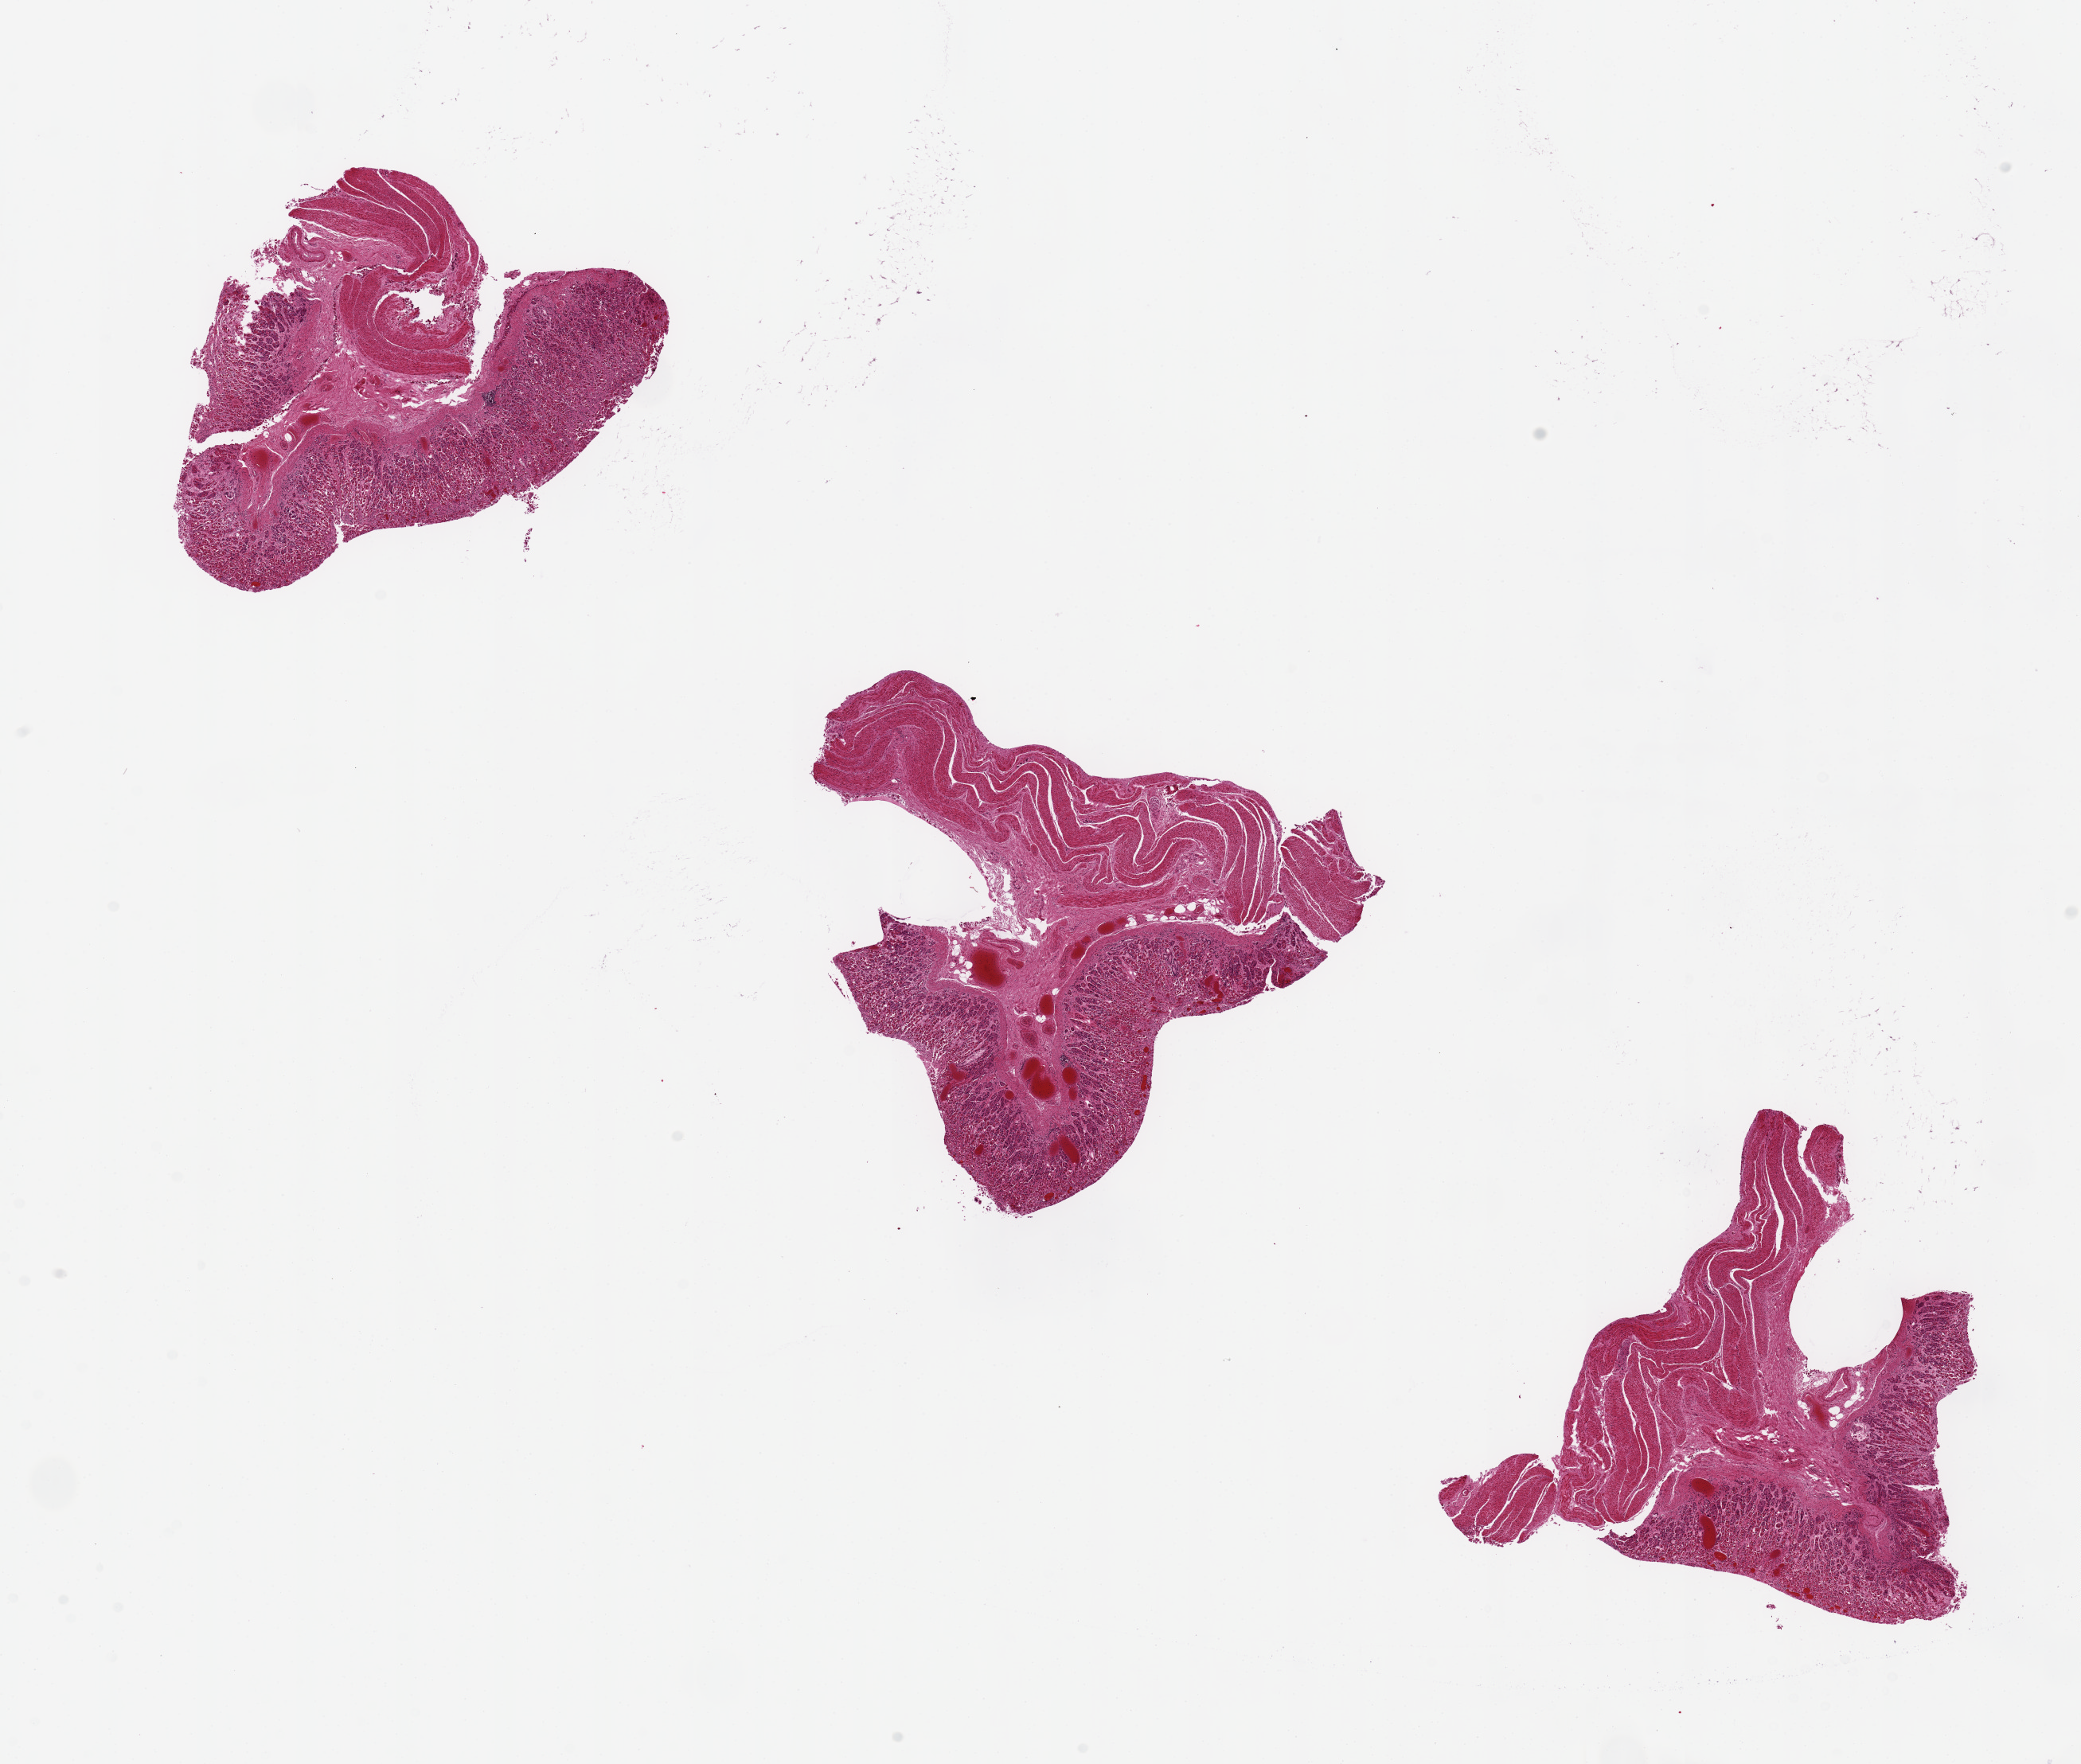
Whole-slide image, H&E stain, shown as a low-resolution overview of the whole scanned area (about 20.7 x 17.5 mm), PAXgene-fixed paraffin-embedded (PFPE) section, target tissue: stomach, donor tissue sample. Donor: female.
* reviewer comment on this tissue sample: Mucosa ~80% autolyzed